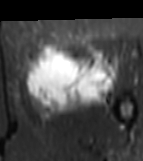
MRI of an extremity soft-tissue mass, one axial slice; STIR; MR volume resampled by the dataset authors to the PET/CT grid (not the native acquisition matrix); 3.27 mm slice thickness; 143 × 161 image matrix, field of view 140 × 157 mm. Female patient. From the clinical record (not read from this slice): histological type: myxofibrosarcoma; grade: intermediate; site of the primary tumour: left thigh.
Annotated regions visible in this slice (expert contour drawn on MRI and transferred to this co-registered scan by the dataset authors):
- gross tumour volume including surrounding oedema: bounding box [x1, y1, x2, y2] px = [24, 44, 118, 120]
- gross tumour volume (mass): [26, 44, 114, 105]